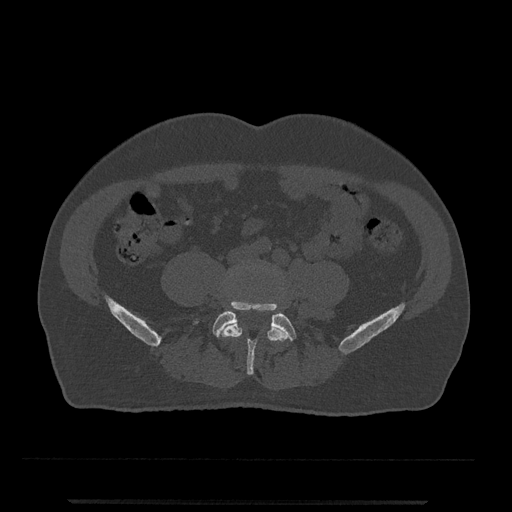
CT including the spine, one axial slice; slice 97 of 797 in the series (ordered by position); reconstruction kernel Br40s/3; 120 kVp; bone window (W 1800 / L 400 HU); 0.5 mm slice thickness; 512 × 512 image matrix, field of view 419 × 419 mm. Patient: male, 63 years. From the clinical record (not read from this slice): primary cancer: prostate.
Structures marked on this image (semi-automatically segmented with operator editing):
- L4 vertebra: box from (x=220, y=264) to (x=289, y=370) px
- L5 vertebra: (x=194, y=302)–(x=297, y=375)